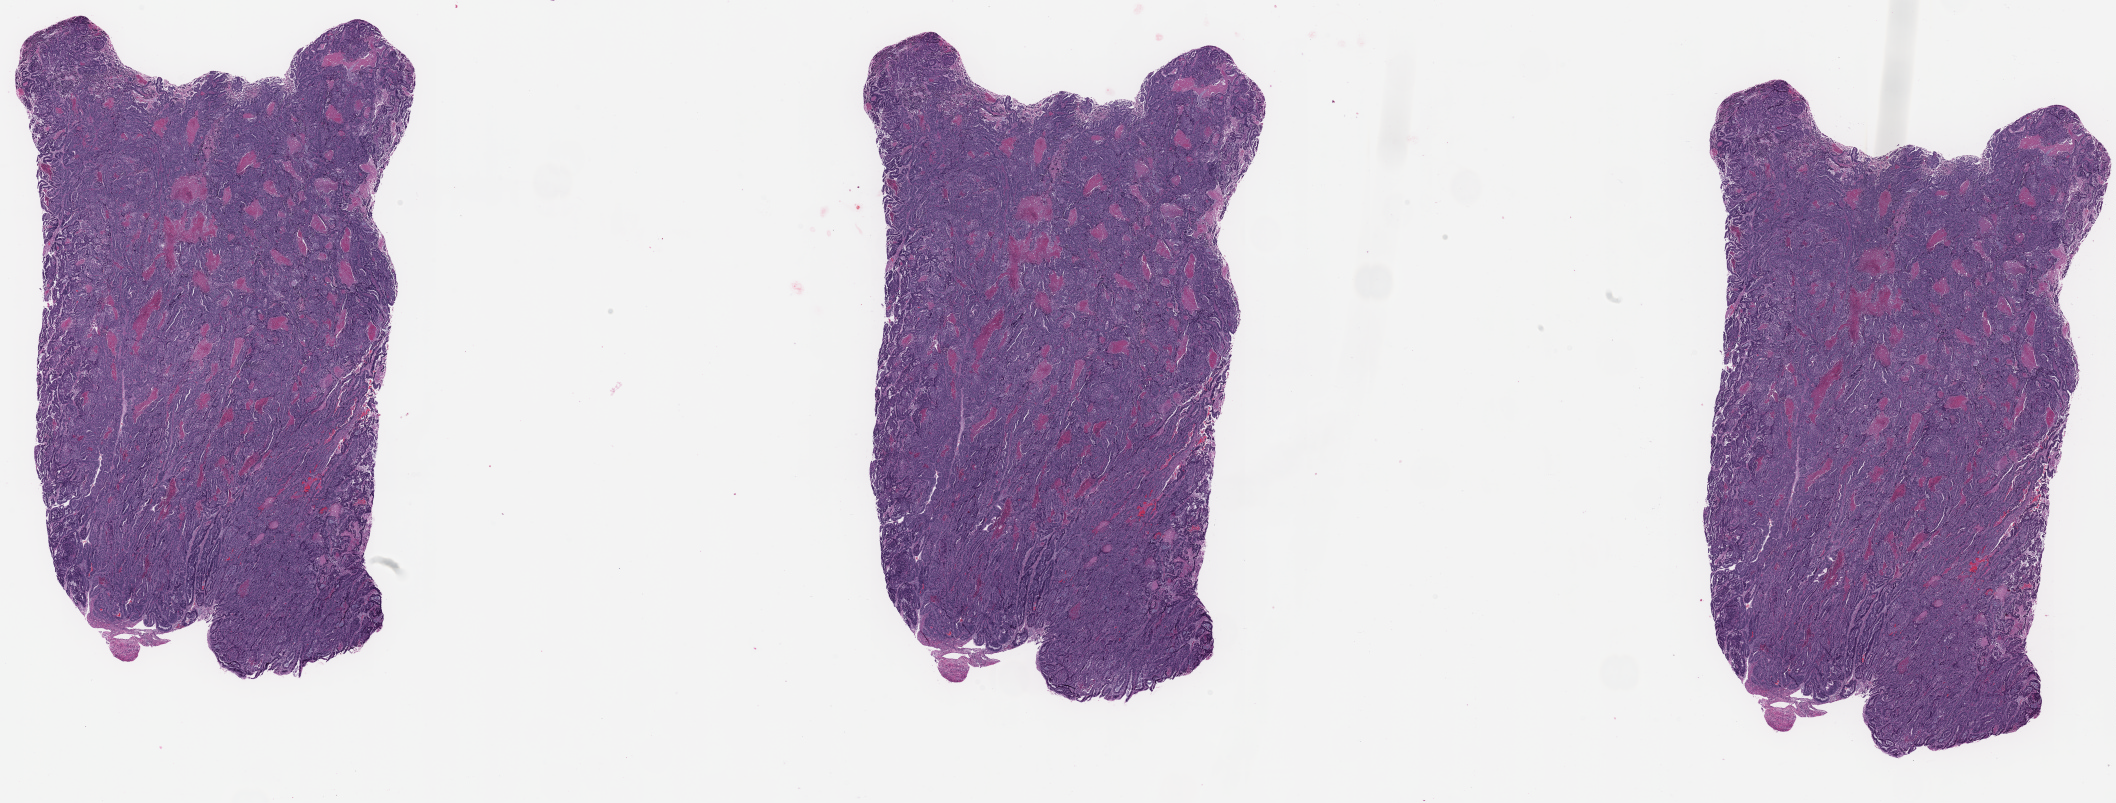
H&E whole-slide image — whole scanned area (about 33.5 x 12.7 mm, acquisition: 20x scan) shown as a low-resolution overview; FFPE section; uterus, primary tumour sample. Female, age 65 years at initial diagnosis. Histologic grade: G2 (moderately differentiated).
Lymph nodes positive (case pathology): 1 of 17 examined. FIGO stage: IIIC1. Diagnosis: Endometrioid adenocarcinoma, NOS (endometrium).